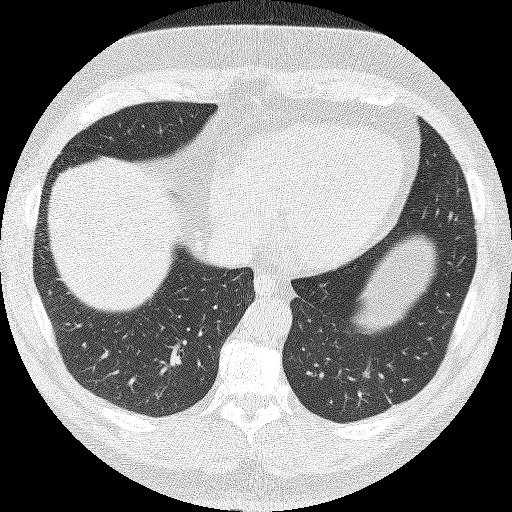
Low-dose screening chest CT, one axial slice. Position 39 of 140 along the scan axis. 120 kVp. Lung window (W 1500 / L -600 HU). 2 mm slice thickness. 512 × 512 image matrix.
Structures marked on this image (outlined manually by an expert reader):
- lesion 1 (tumor, lower lobe of left lung): bounding box <363,371,370,378> (left, top, right, bottom; pixels)